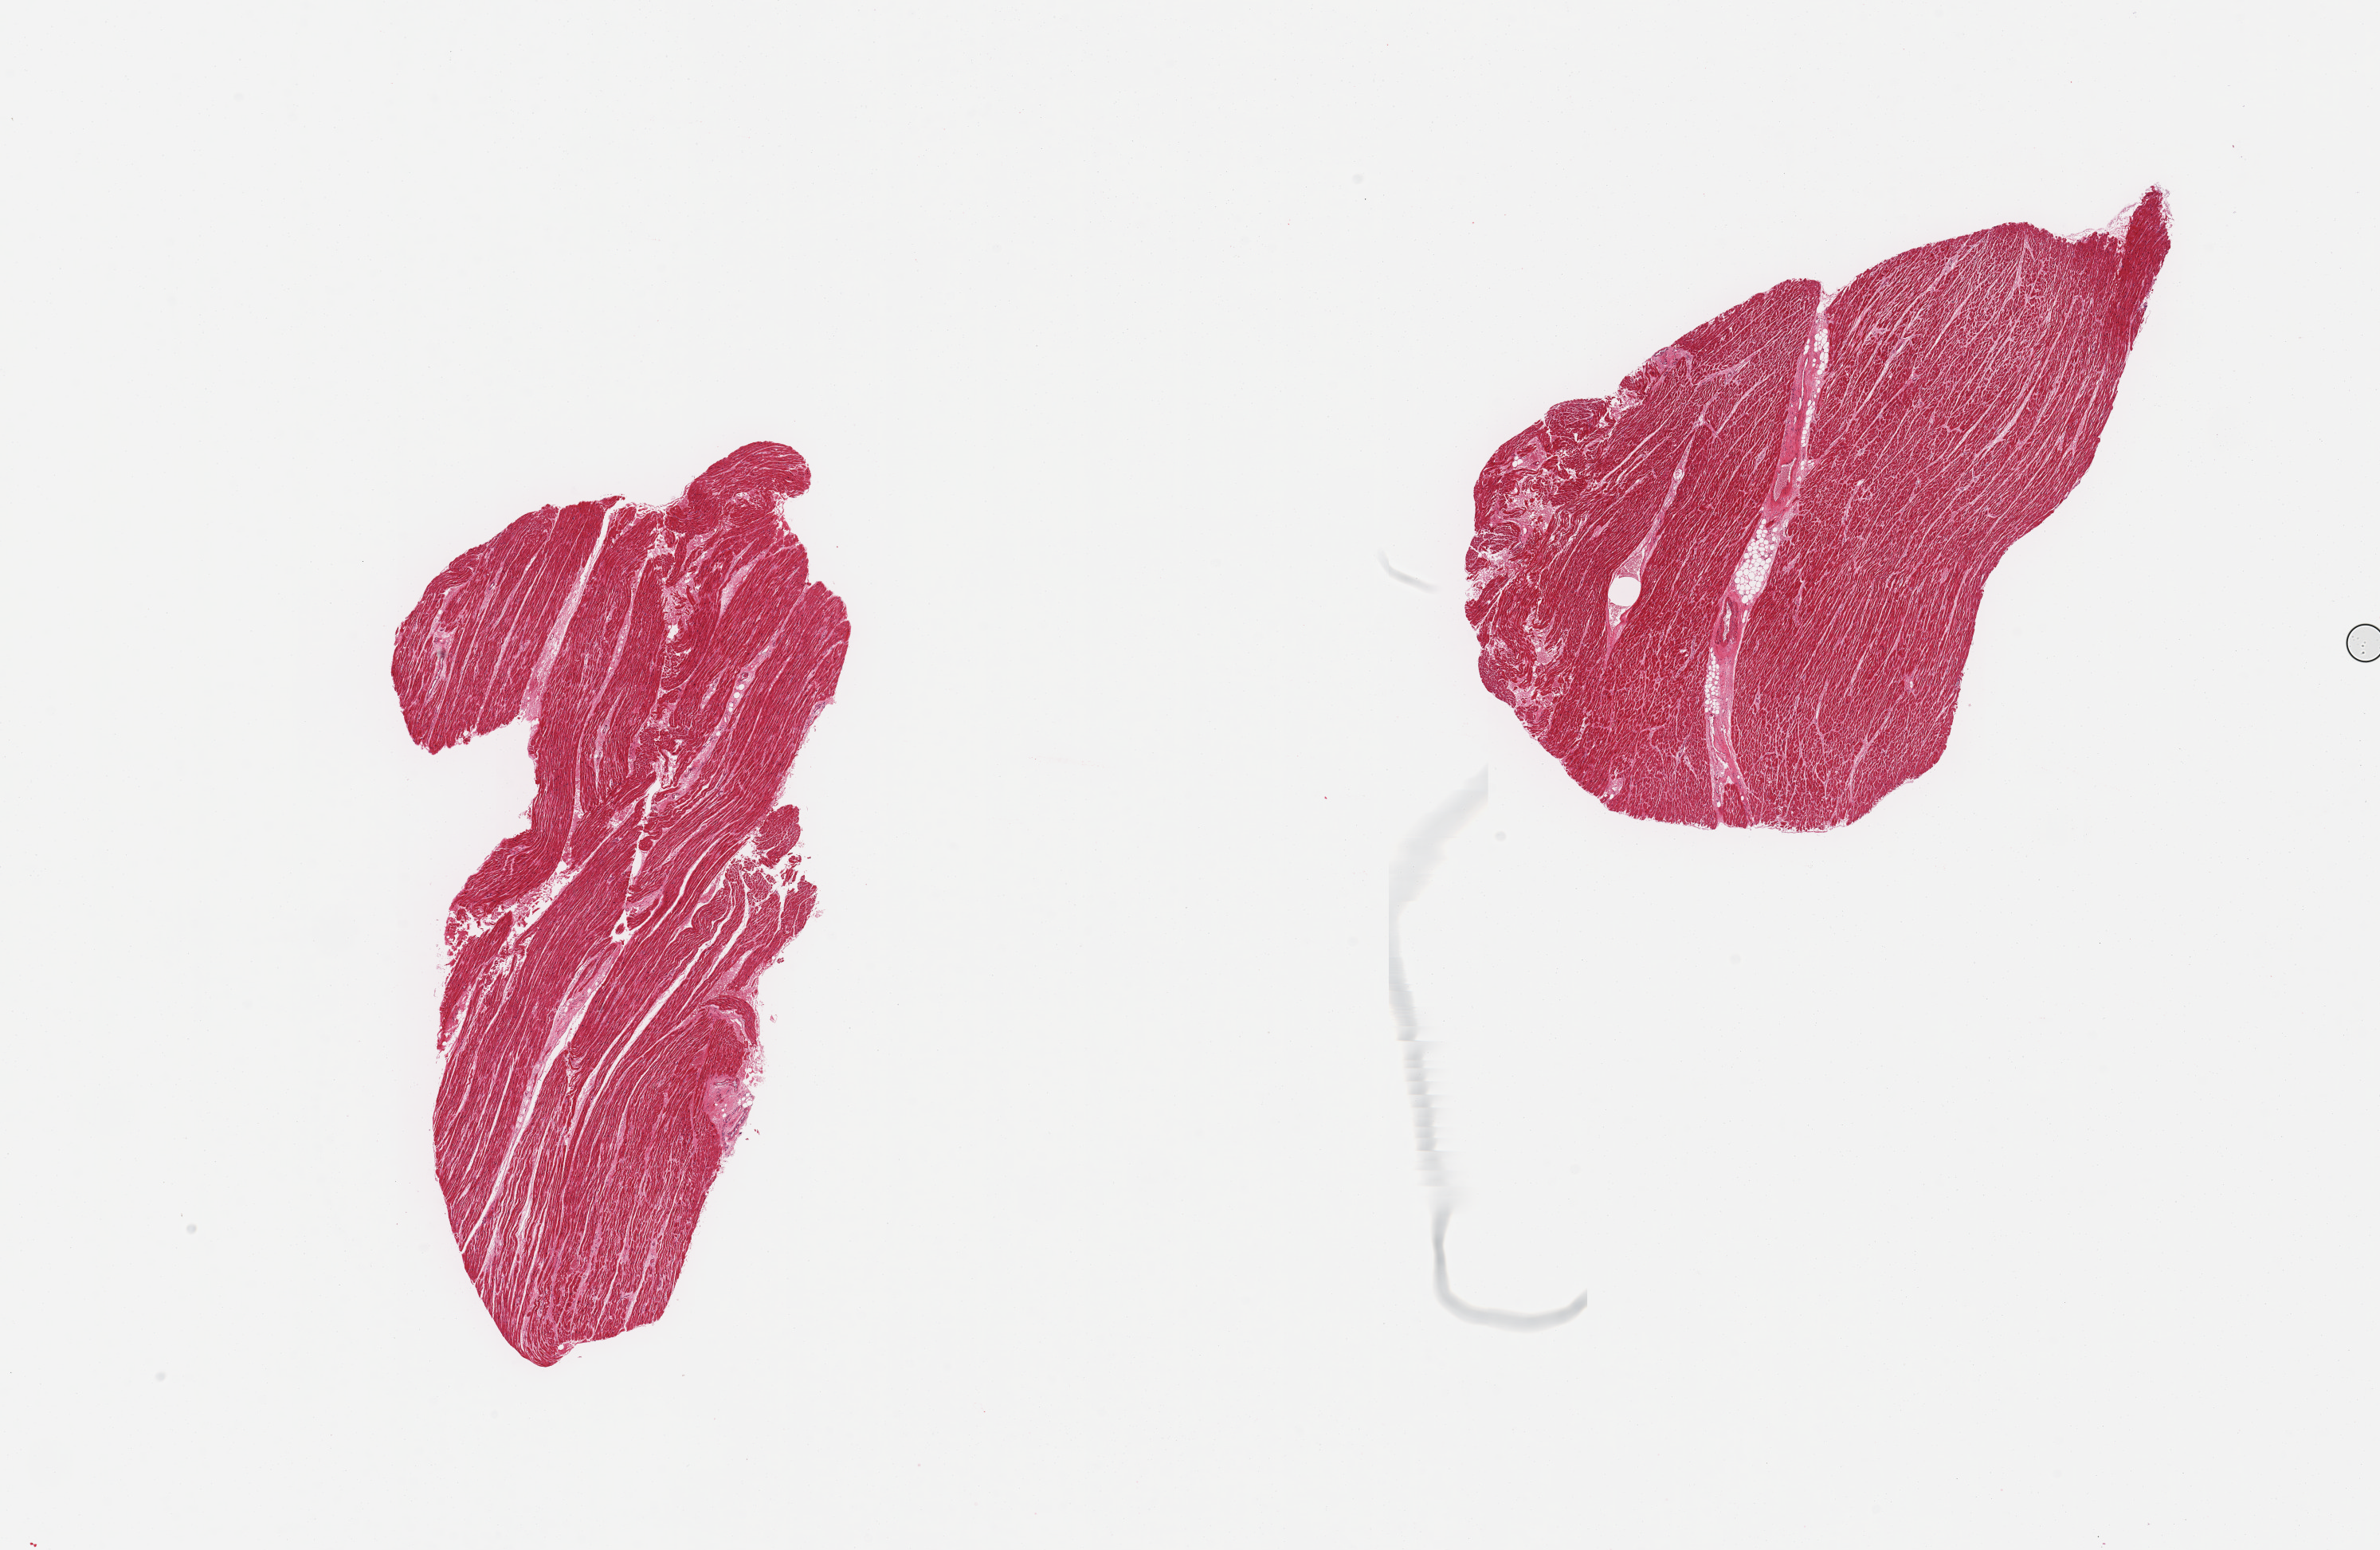
Haematoxylin and eosin whole-slide image — shown as a low-resolution overview of the whole scanned area (about 23.6 x 15.4 mm); PAXgene-fixed, paraffin-embedded tissue; sampled site (target tissue): heart; tissue donor sample. Donor: male.
Review note (as recorded): 2 pieces, moderate interstitial fibrosis/chronic ischemic changes.